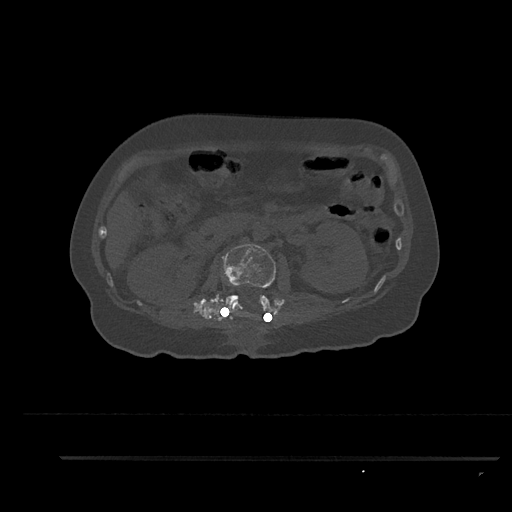
CT including the spine, one axial slice; slice 183 of 797 in the series (ordered by position); reconstruction kernel Br40s/3; 120 kVp; bone window (W 1800 / L 400 HU); 0.5 mm slice thickness; 512 × 512 image matrix, field of view 408 × 408 mm. Female patient, age 44 years. Case-level facts recorded for this patient, not image findings: primary cancer: renal; vertebrae with lytic lesions (as recorded): L1.
Annotated regions visible in this slice (semi-automatically segmented with operator editing):
- L1 vertebra: bounding box <233,285,238,307> (left, top, right, bottom; pixels)
- L2 vertebra: <224,244,277,320>